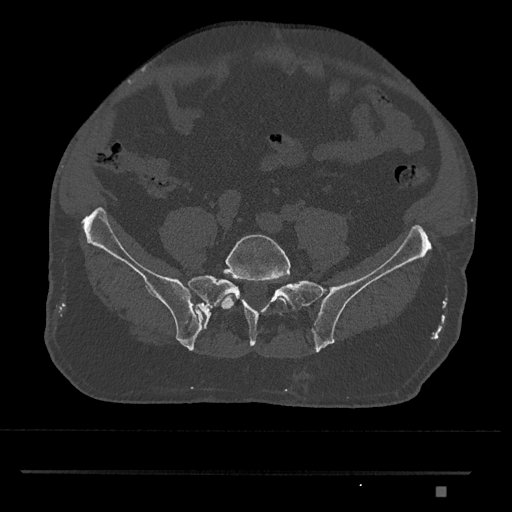
CT including the spine, one axial slice; slice 529 of 1134 in the series (ordered by position); reconstruction kernel Br40s/3; bone window (W 1800 / L 400 HU); 0.5 mm slice thickness; 512 × 512 image matrix. Male patient, age 65 years. From the clinical record (not read from this slice): primary cancer: prostate.
Structures marked on this image (semi-automatic segmentation, software-assisted and operator-edited):
- L5 vertebra: box from (x=221, y=234) to (x=291, y=312) px